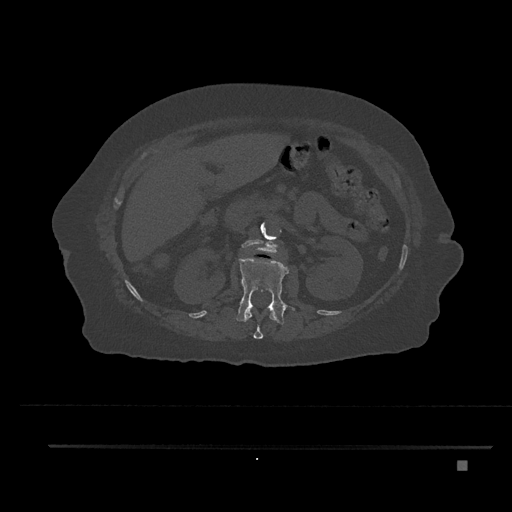
CT including the spine, one axial slice. Slice 225 of 797 in the series (ordered by position). Reconstruction kernel Br40s/3. 120 kVp. Bone window (W 1800 / L 400 HU). 0.5 mm slice thickness. 512 × 512 image matrix, field of view 437 × 437 mm. Patient: female, 76 years. Case-level facts recorded for this patient, not image findings: primary cancer: lung.
Outlined on this slice (semi-automatic segmentation, software-assisted and operator-edited):
- L1 vertebra: box from (x=236, y=255) to (x=289, y=325) px
- L2 vertebra: (x=242, y=239)–(x=279, y=255)
- T12 vertebra: (x=243, y=308)–(x=277, y=339)